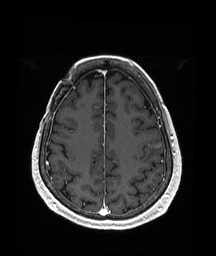
Brain MRI from a brain-tumour surgery series, one axial slice; position 61 of 176 along the scan axis; T1-weighted post-contrast; 1 mm slice thickness; 216 × 256 image matrix, field of view 211 × 250 mm. Case-level facts recorded for this patient, not image findings: histopathology: Metastatic Malignant Melanoma; tumour location: Left Frontal.
Structures marked on this image (expert manual segmentation):
- tumour: bounding box [x1, y1, x2, y2] px = [154, 143, 161, 148]